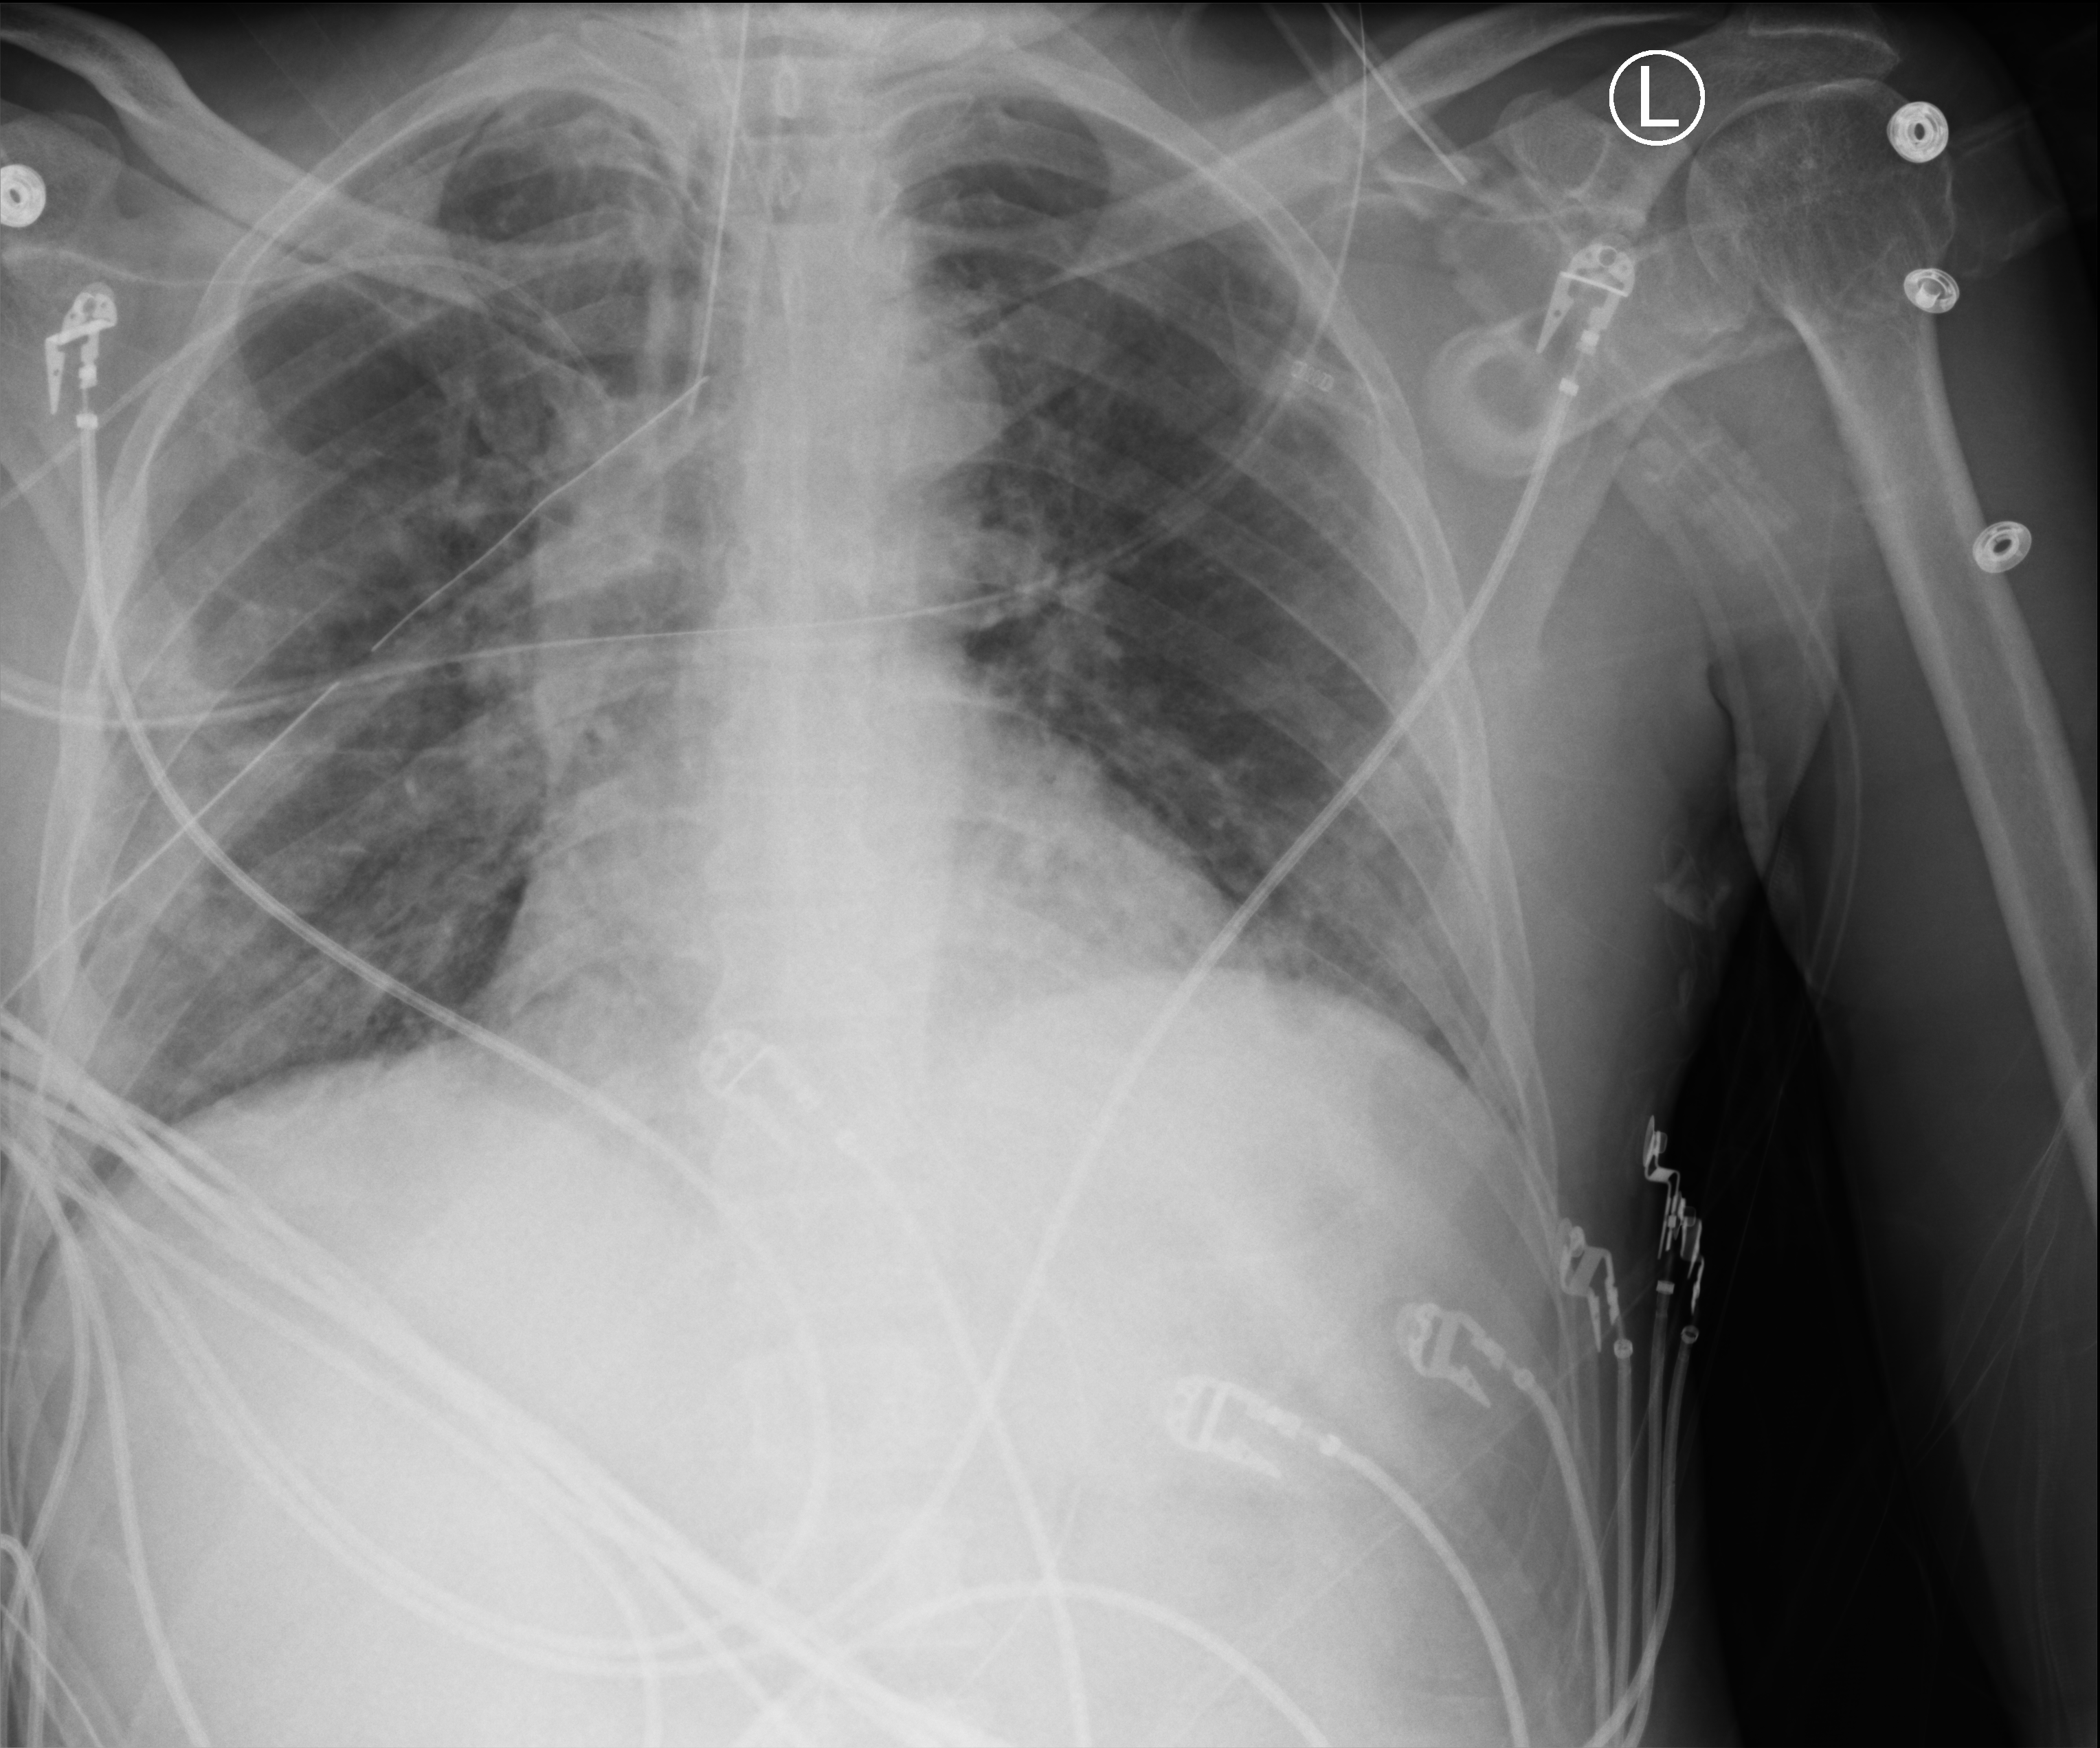
Chest X-ray (portable); anteroposterior (AP) projection. Patient hospitalised with COVID-19; male, aged 18–59 years.
From the hospital-stay record, not from the radiograph (when in the stay this image was taken is not recorded): length of hospital stay: 41 days.